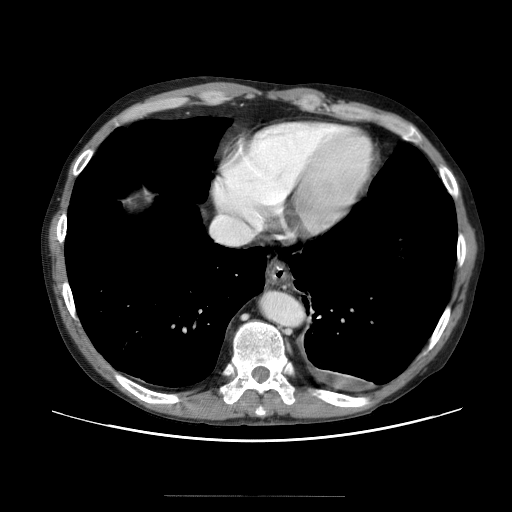
Contrast-enhanced abdominal CT (liver protocol), one axial slice. Slice 61 of 69 in the series (ordered by position). Soft-tissue window (W 400 / L 40 HU). 2.5 mm slice thickness. 512 × 512 image matrix, field of view 380 × 380 mm. From the clinical record (not read from this slice): diagnosis: hepatocellular carcinoma (patient treated with transarterial chemoembolisation; whether this scan precedes or follows treatment is not stated here); TNM stage (as recorded): Stage-IVB; Child-Pugh class: B; tumour differentiation: poorly differentiated; tumour nodularity: multinodular.
Annotated regions visible in this slice (semi-automatically segmented with operator editing):
- liver parenchyma outside the tumour (the mass and vessels are separate outlines, so this box may not span the whole liver): box from (x=104, y=182) to (x=160, y=230) px